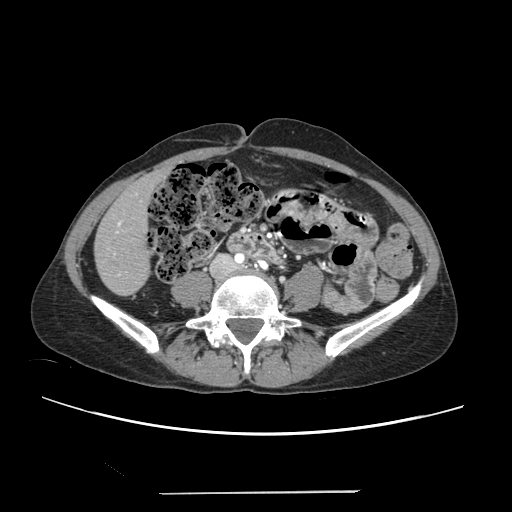
Contrast-enhanced abdominal CT, one axial slice. Slice 41 of 240 in the series (ordered by position). 120 kVp. Intravenous contrast given. Soft-tissue window (W 400 / L 40 HU). 512 × 512 image matrix. Female patient, age 60 years. Case-level facts recorded for this patient, not image findings: diagnosis: colorectal cancer liver metastases, imaged before liver resection; multiple liver metastases: no; largest metastasis: 1.5 cm; disease in both lobes: no.
Annotated regions visible in this slice (outlined manually by an expert reader):
- liver: bounding box <96,172,164,295> (left, top, right, bottom; pixels)
- planned liver remnant (the part of the liver to remain after resection): <96,172,164,295>
- portal vein (with intrahepatic branches): <108,194,137,275>